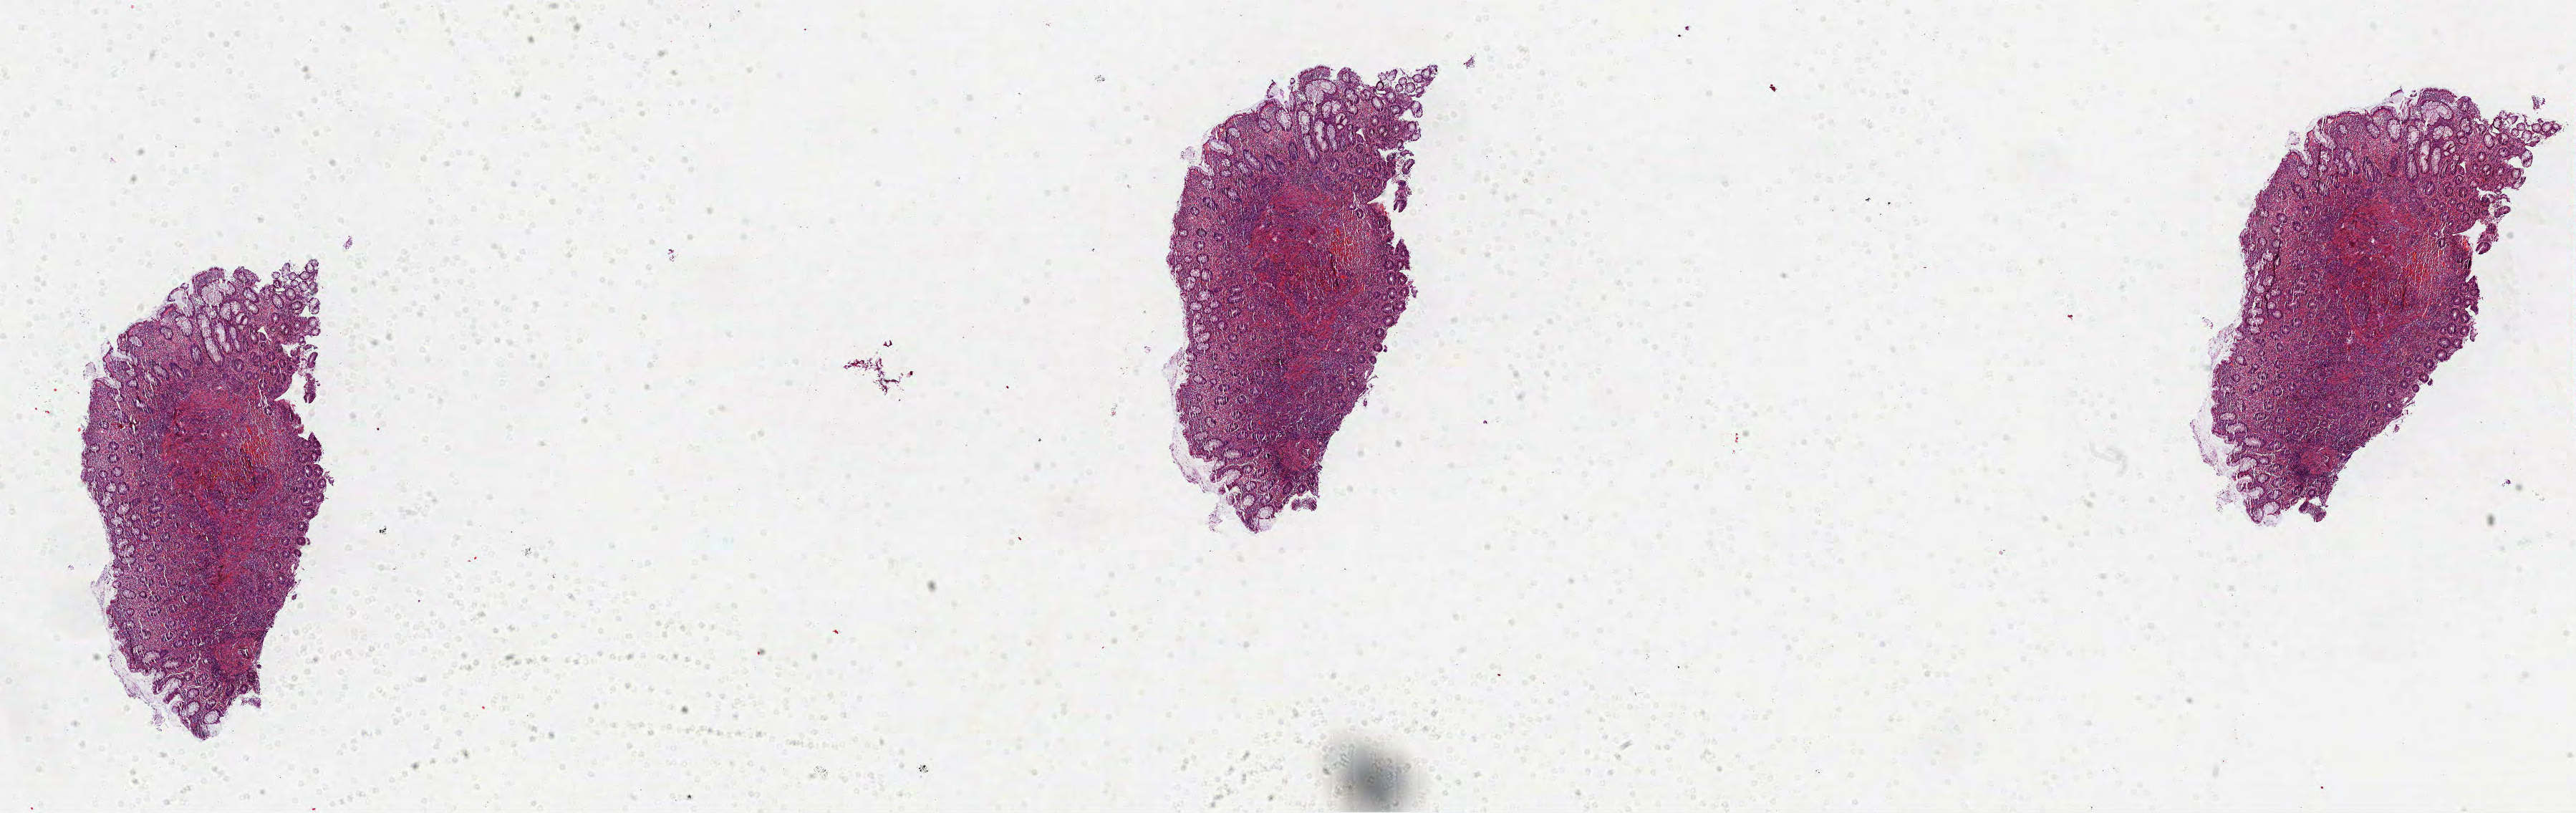
Digitized H&E-stained tissue section (whole slide), shown as a low-resolution overview of the whole scanned area (about 29.0 x 9.2 mm, from a 40x scan), formalin-fixed paraffin-embedded (FFPE) diagnostic section, colon, primary tumour sample. Female patient; age at initial diagnosis 73 years.
Histologic diagnosis: Adenocarcinoma, NOS (ascending colon). AJCC pathologic stage: IIB (6th edition). Lymph nodes positive (case pathology): 0 of 16 examined.